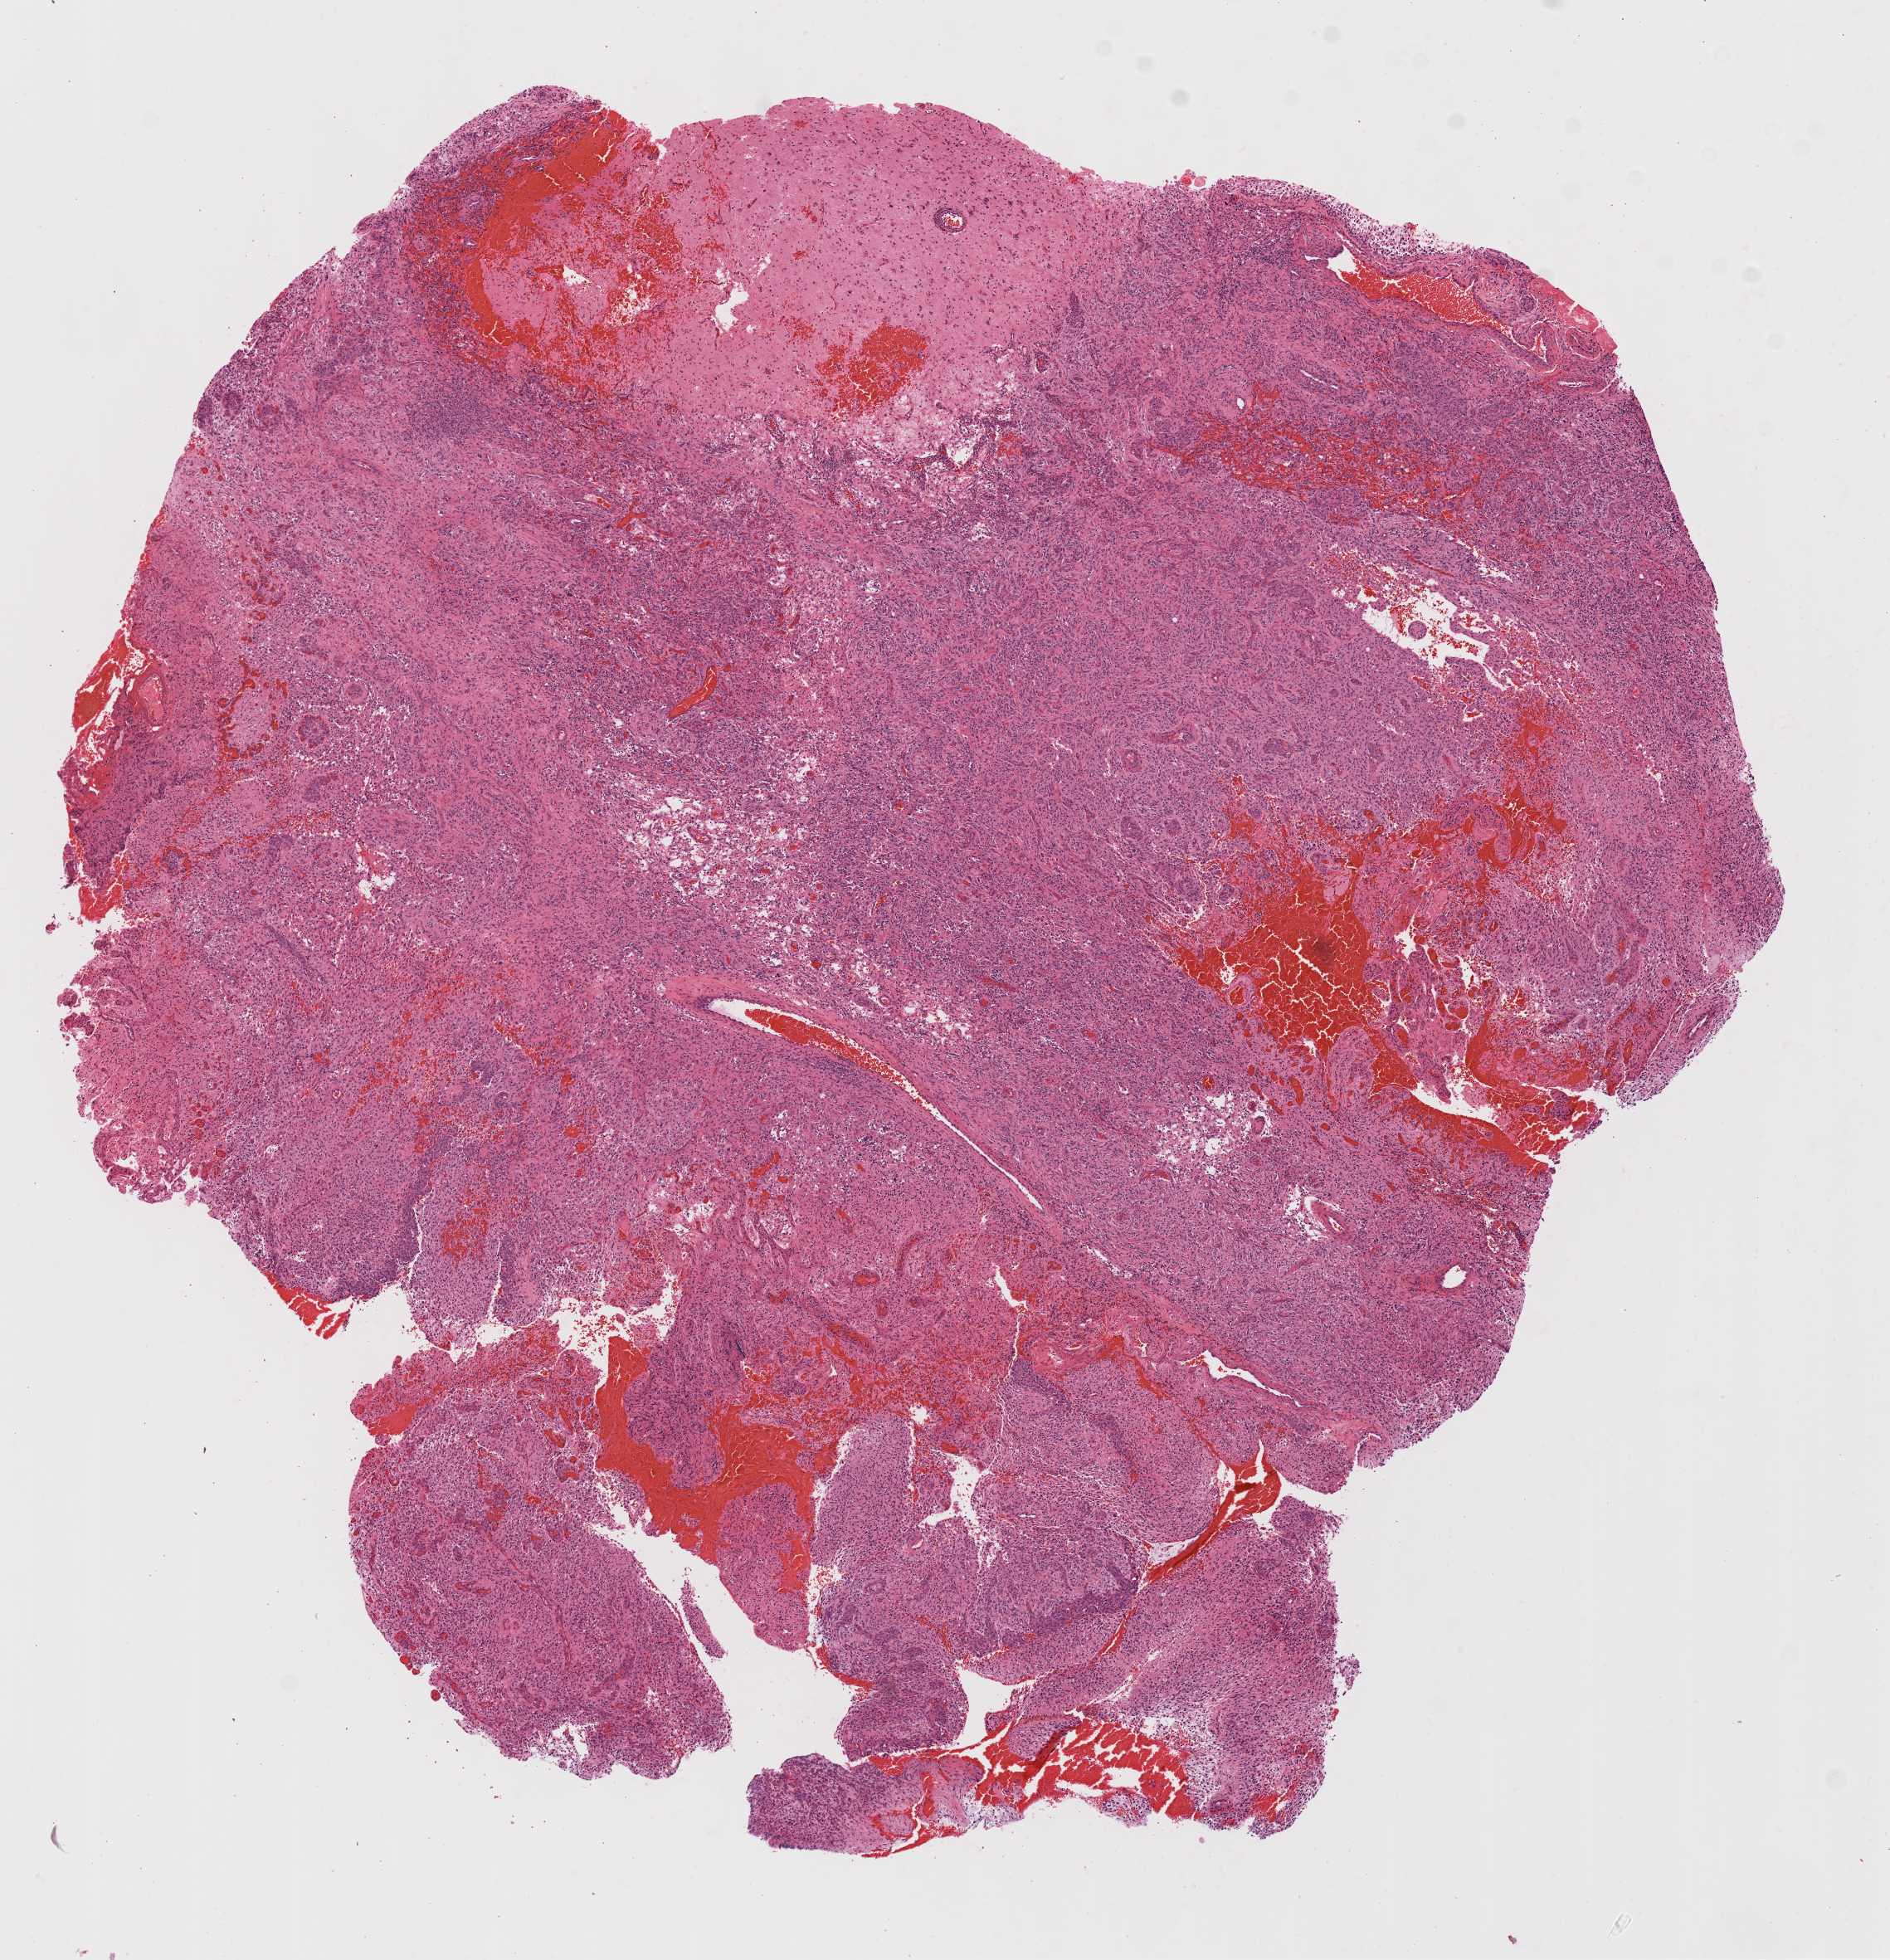
Whole-slide histology image, H&E-stained, low-resolution overview of the scanned area, about 9.2 x 9.5 mm (from a 20x scan), formalin-fixed paraffin-embedded (FFPE) diagnostic section, primary tumour sample from the brain. Male, age 67 years at initial diagnosis.
Diagnosis: Glioblastoma.